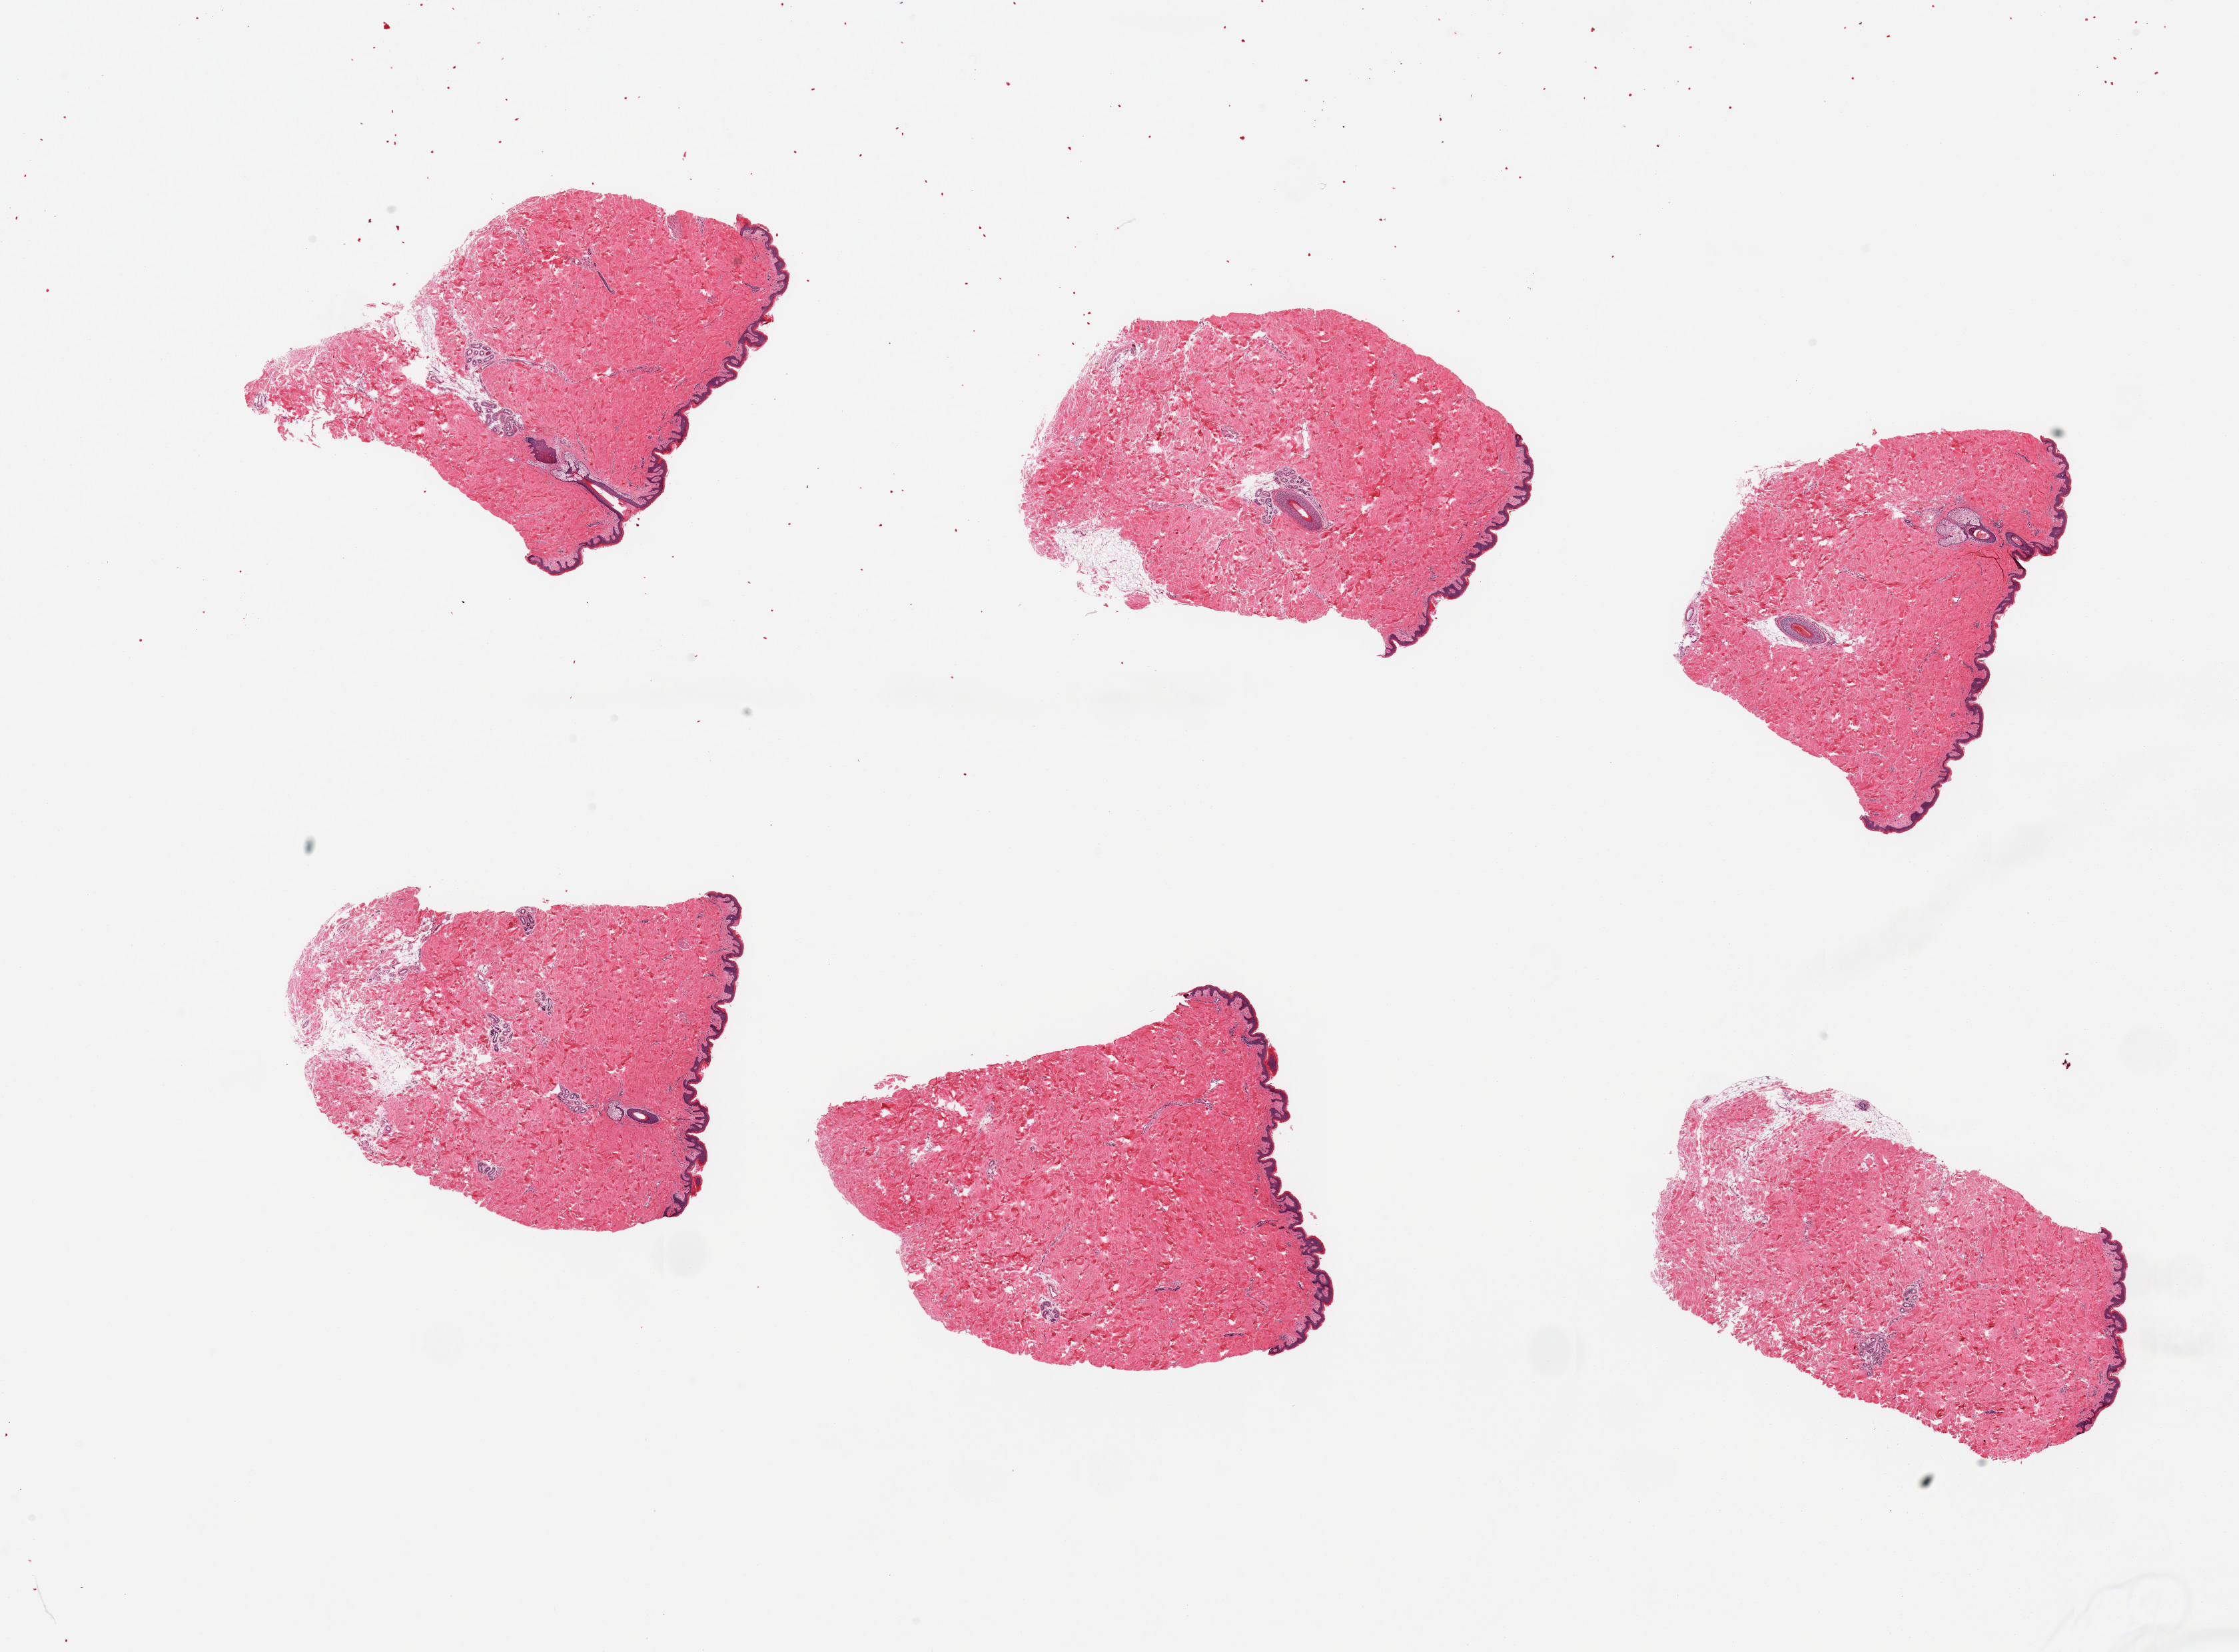
Whole-slide image, H&E stain, brightfield, whole scanned area (about 26.6 x 19.6 mm) shown as a low-resolution overview, PAXgene-fixed paraffin-embedded (PFPE) section, section of skin of suprapubic region (target tissue), tissue donor sample. Male donor.
Pathologist's review note for this sample: 6 pieces, minimal adherent fat. Squamous epithelium is ~60 microns.